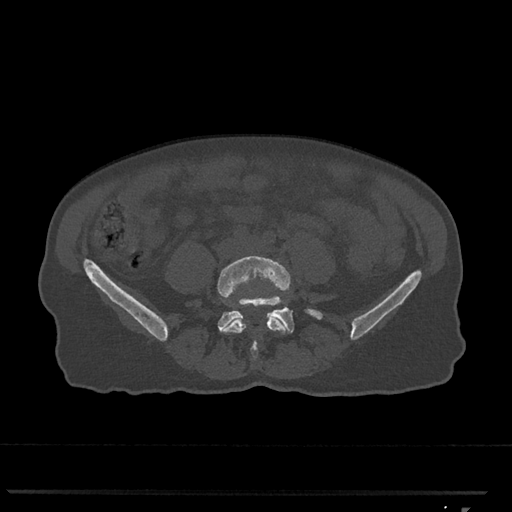
CT including the spine, one axial slice; position 180 of 793 along the scan axis; reconstruction kernel Br40s/3; 120 kVp; bone window (W 1800 / L 400 HU); 0.5 mm slice thickness; 512 × 512 image matrix, field of view 380 × 380 mm. Patient: female, 62 years. From the clinical record (not read from this slice): primary cancer: renal.
Outlined on this slice (semi-automatically segmented with operator editing):
- L4 vertebra: bounding box [x1, y1, x2, y2] px = [217, 256, 291, 358]
- L5 vertebra: [218, 296, 323, 333]